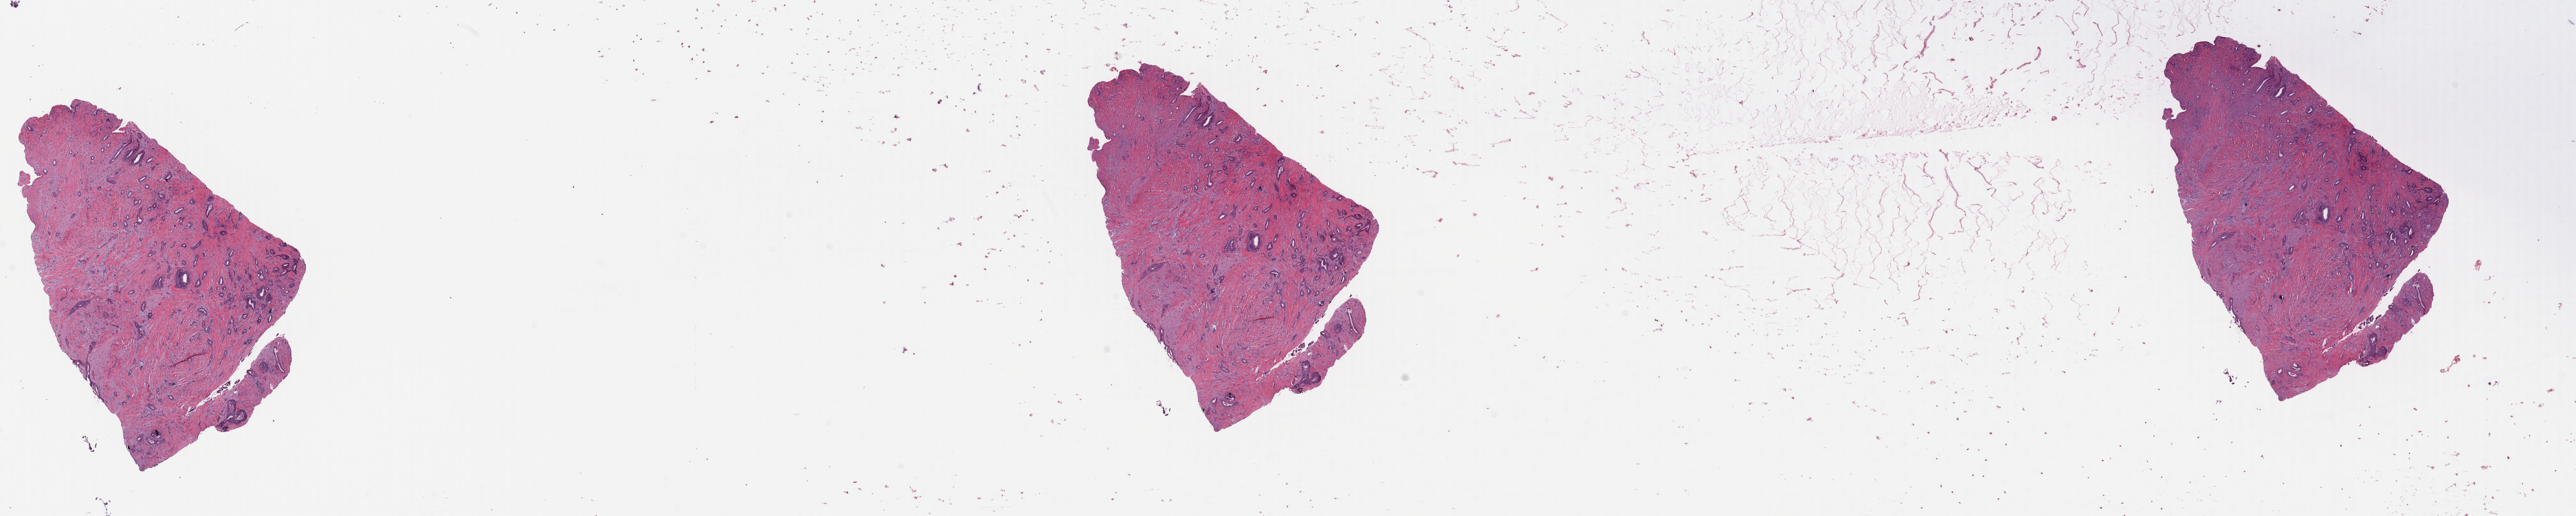
Digitized H&E-stained tissue section (whole slide) — whole scanned area (about 29.6 x 5.9 mm, slide scanned at 40x) shown as a low-resolution overview. Formalin-fixed paraffin-embedded (FFPE) diagnostic section. Primary tumour sample from the breast. Female, age 47 years at initial diagnosis.
* histologic diagnosis: Infiltrating duct carcinoma, NOS
* AJCC pathologic stage: IIA (7th edition)